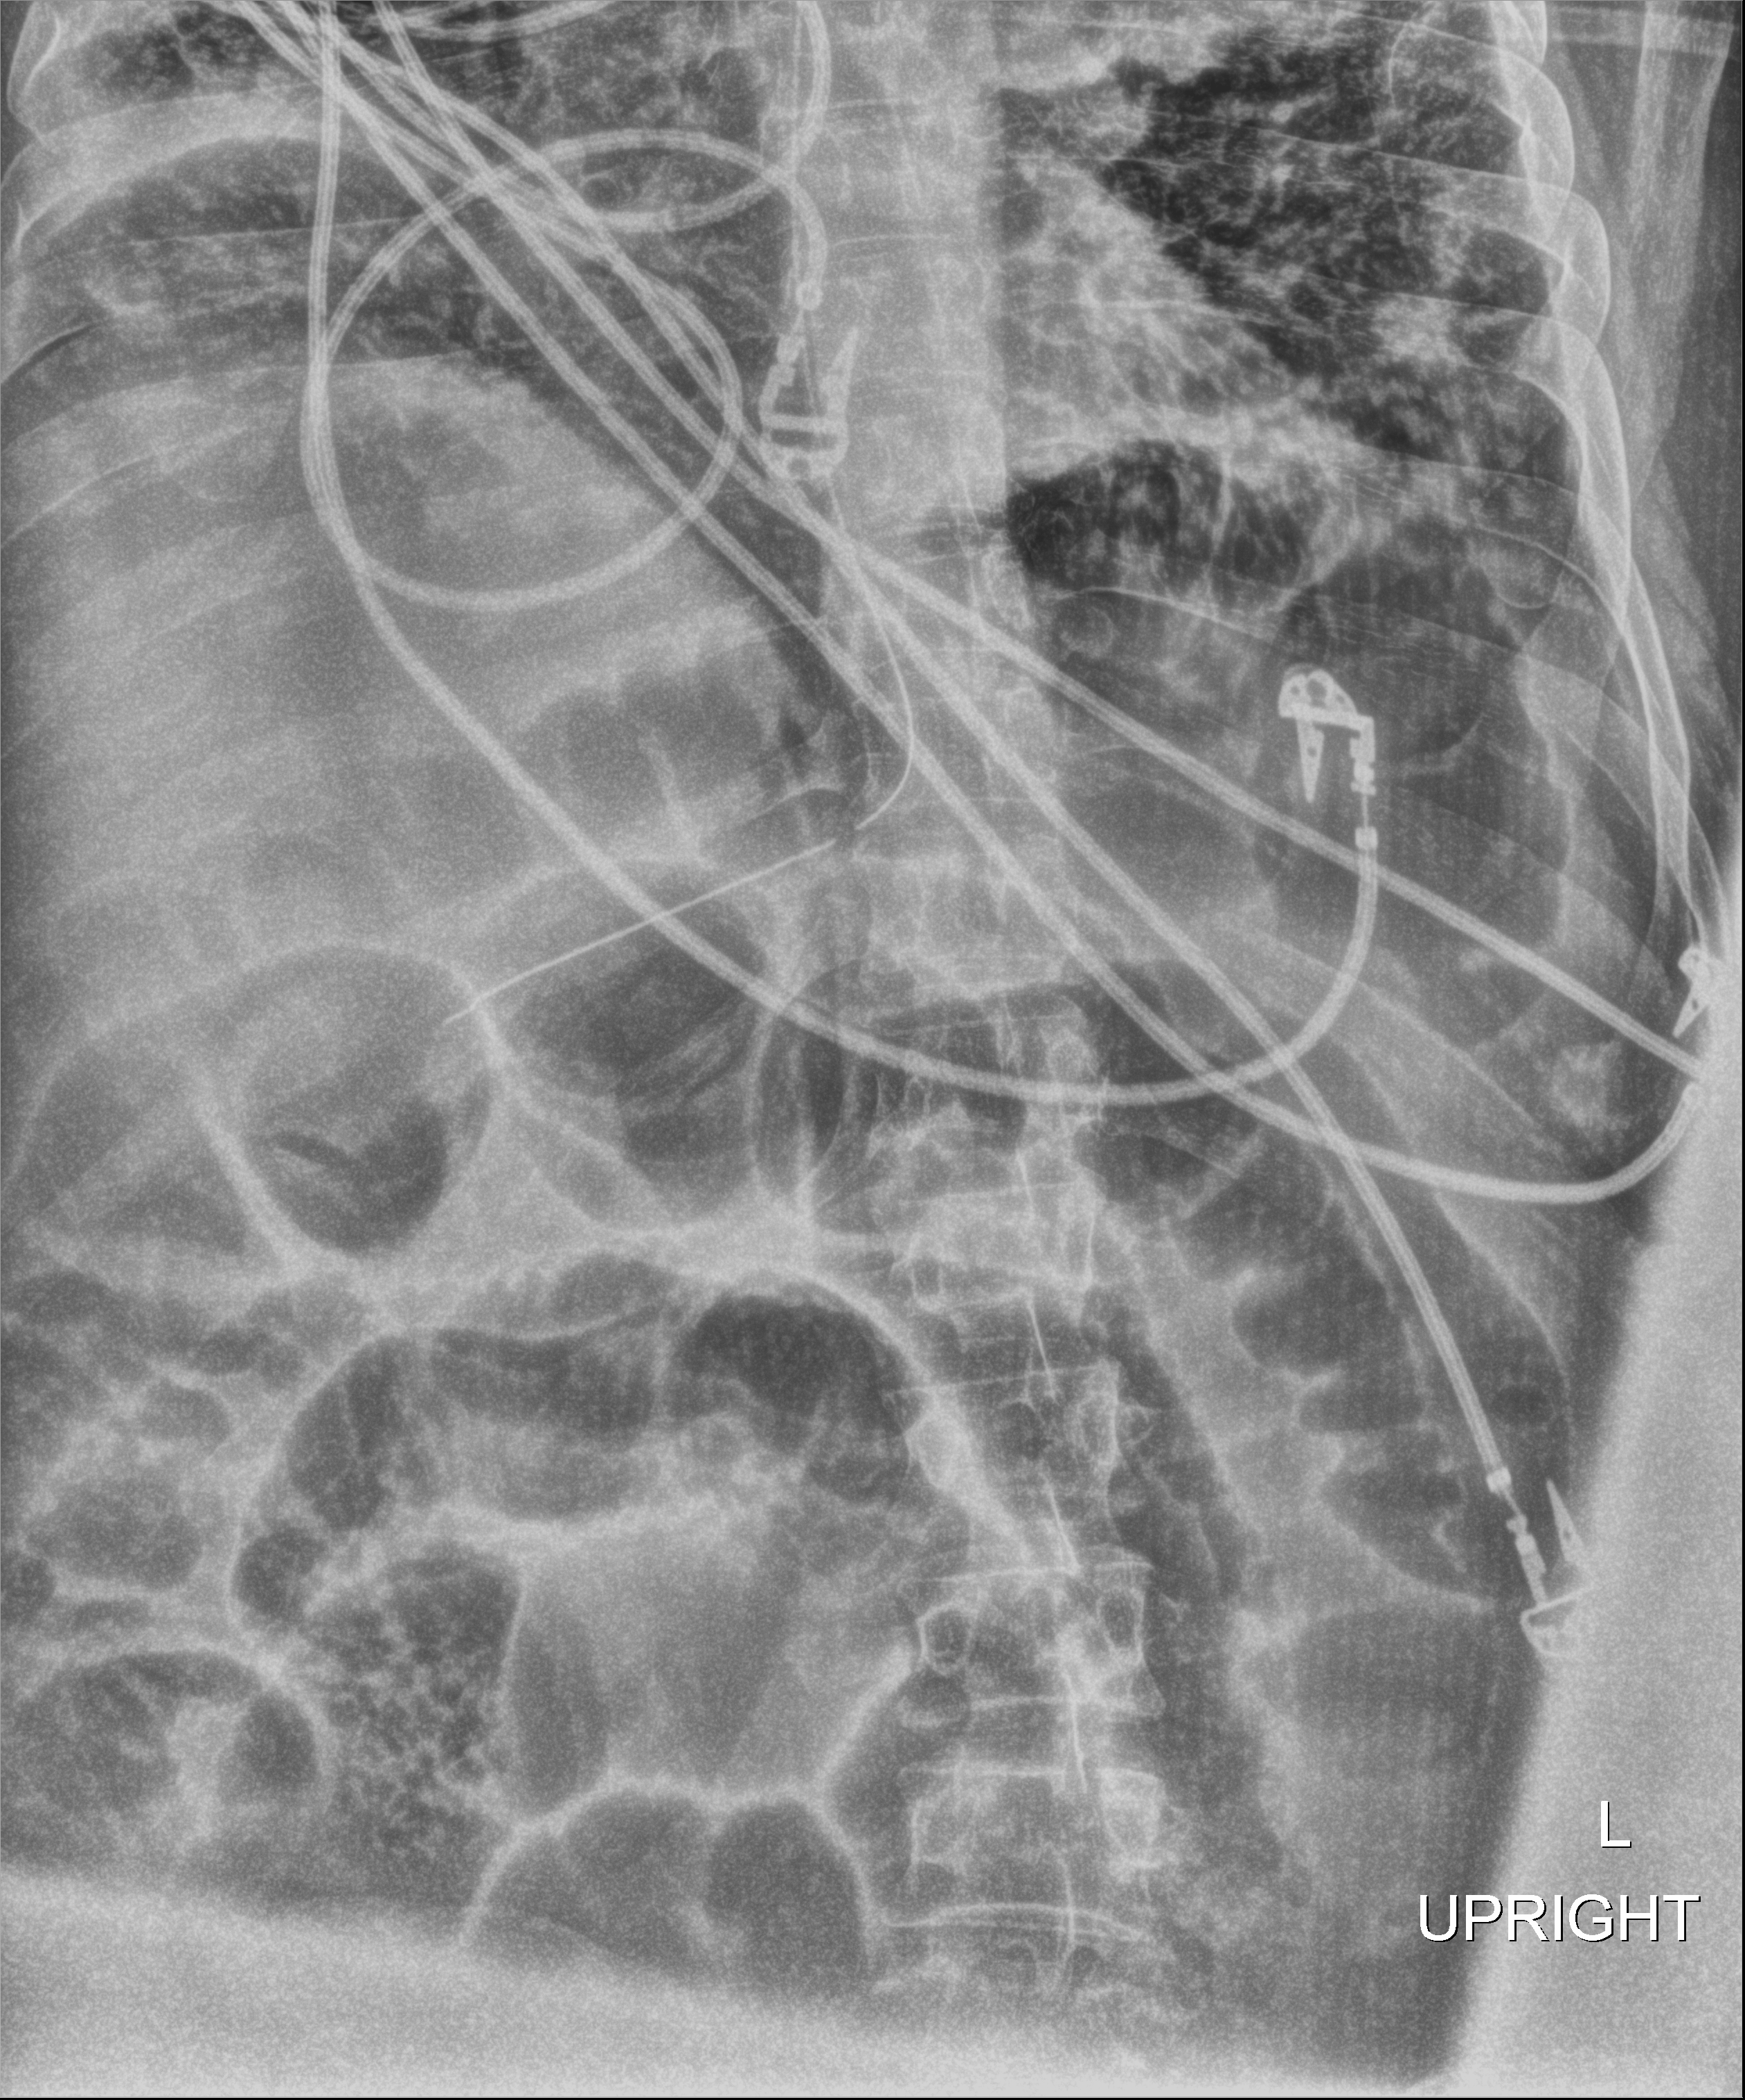
Abdomen X-ray (portable); anteroposterior (AP) projection. Patient hospitalised with COVID-19, aged 18–59 years.
Admission-level facts for this patient (not findings on this image; timing relative to this image not recorded): diabetes (admission record): no; hypertension (admission record): yes; admitted to intensive care during this hospital stay: yes.